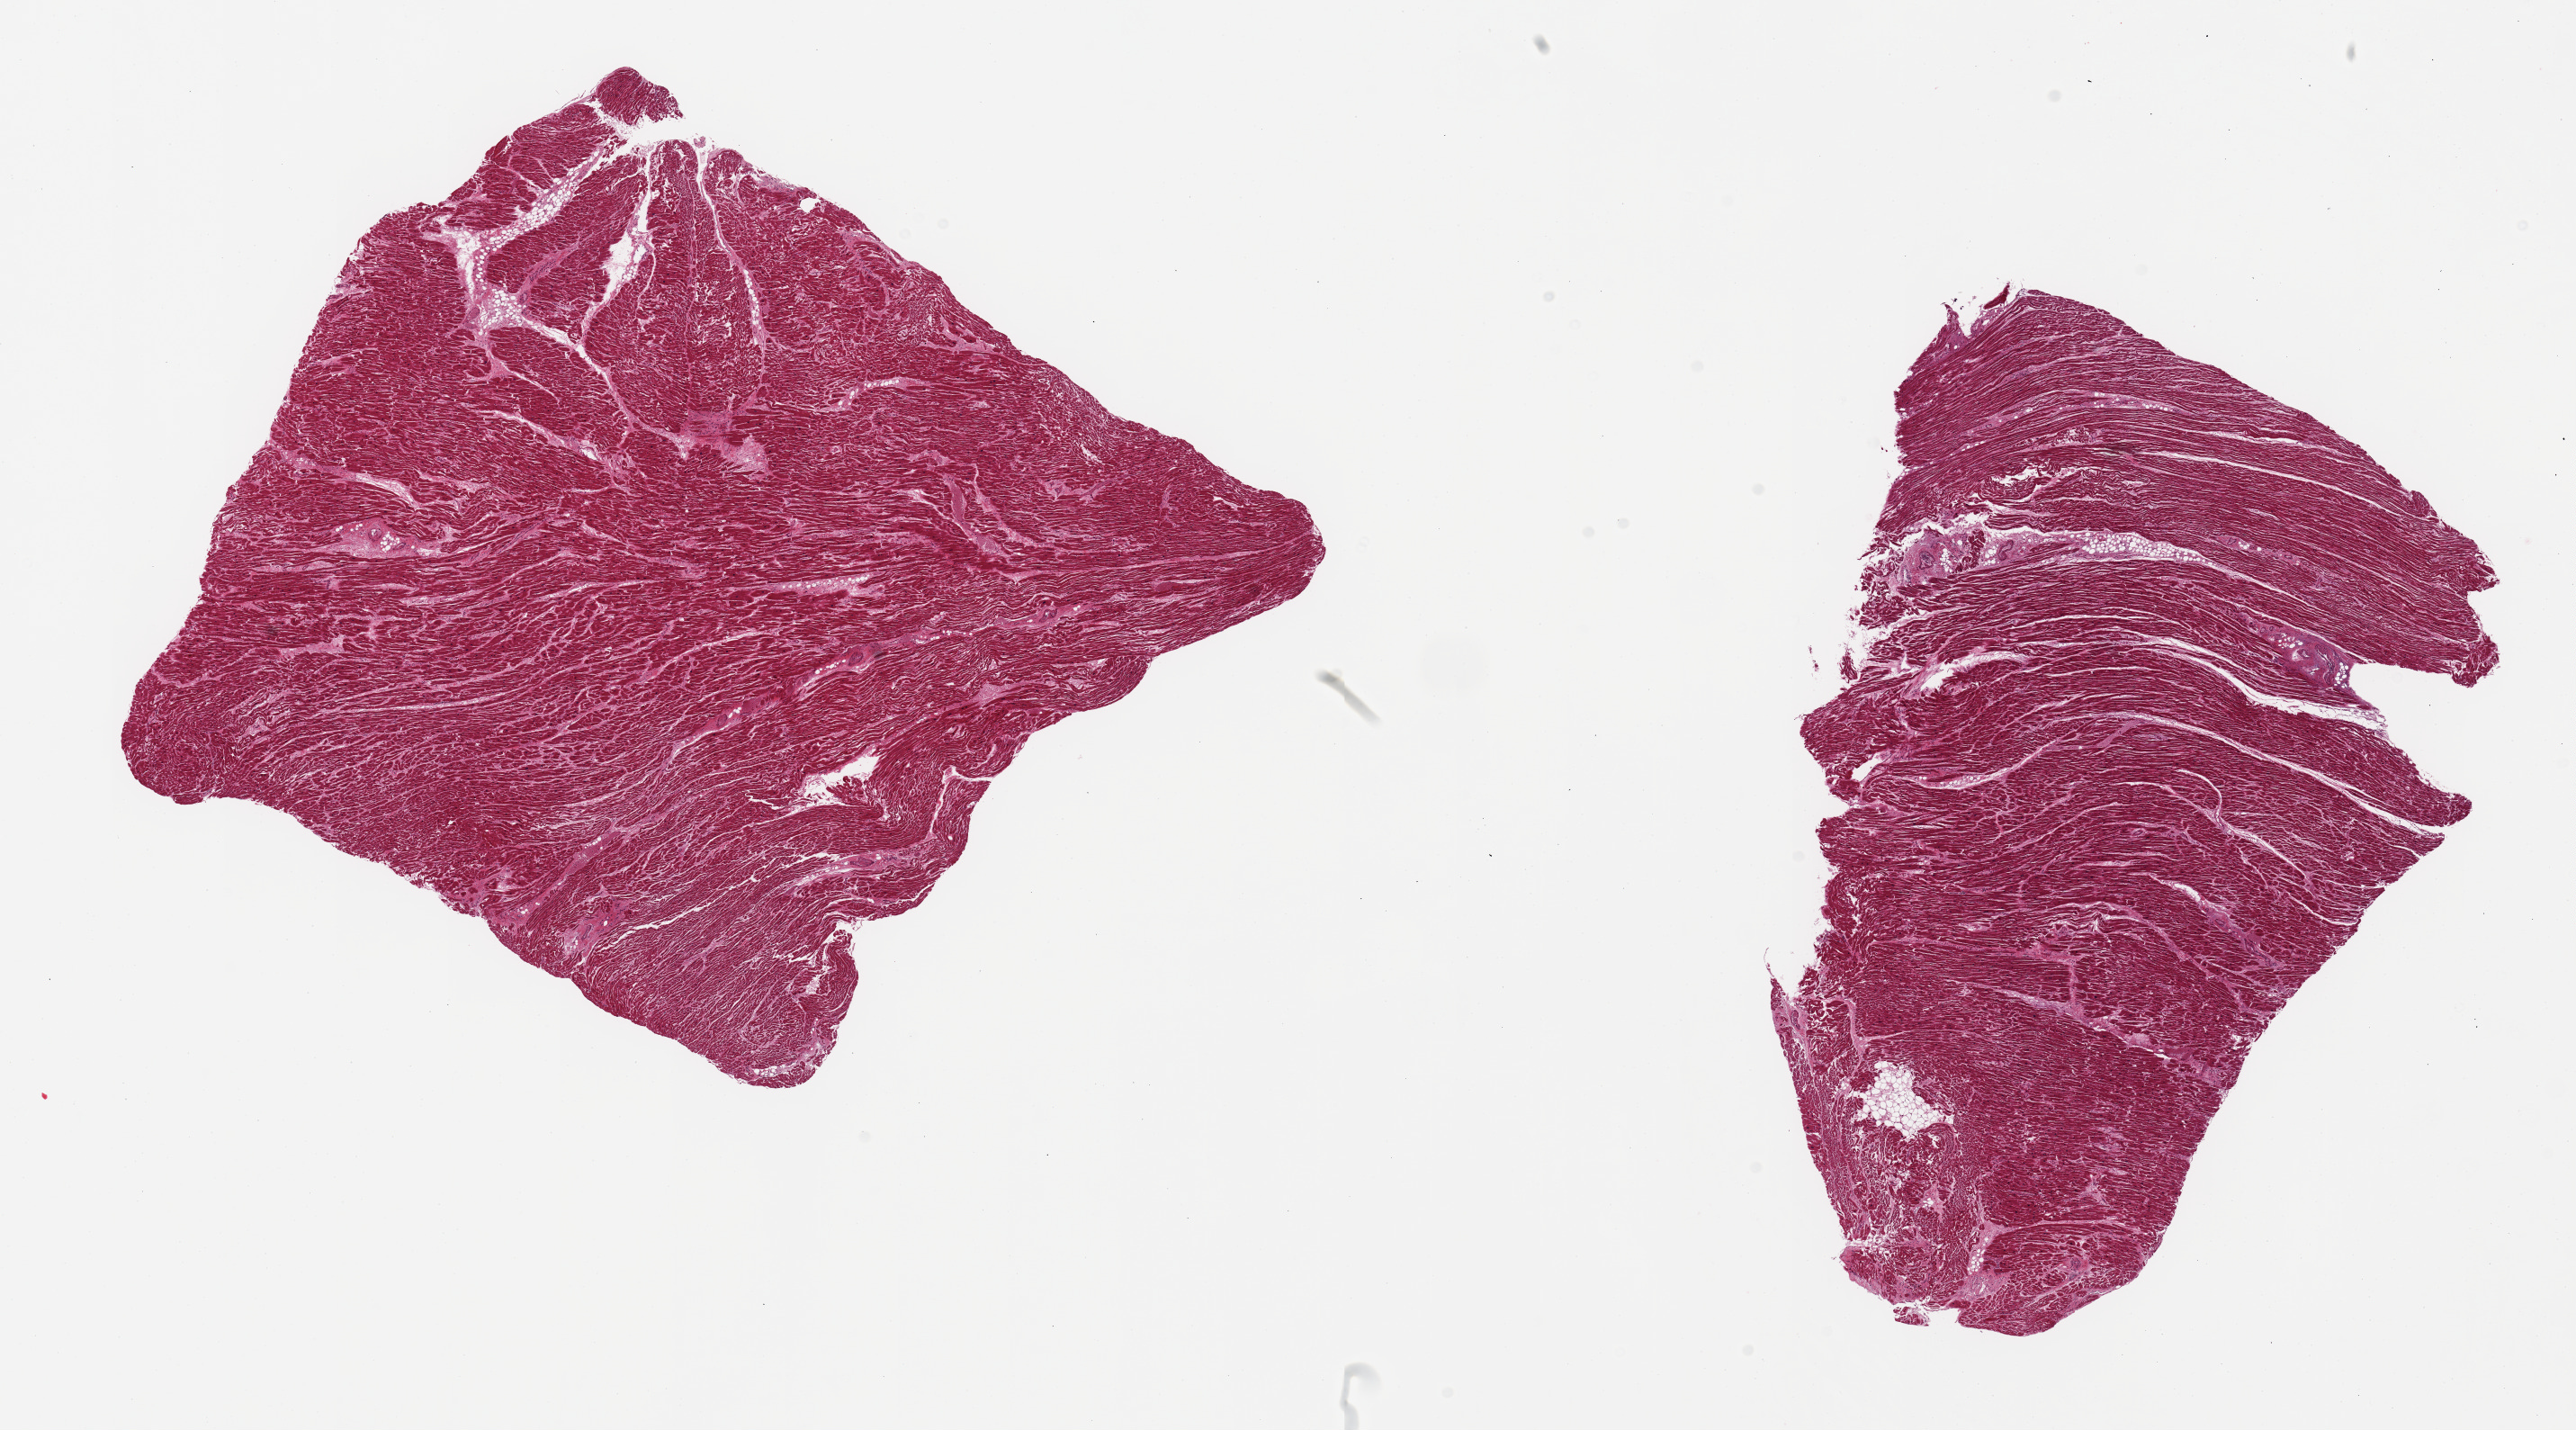
Digitized hematoxylin and eosin (H&E)-stained section, brightfield, a low-resolution overview of the entire scanned area, about 22.6 x 12.6 mm (from a 20x scan); PAXgene-fixed paraffin-embedded (PFPE) section; sampled site (target tissue): heart; tissue donor sample. Donor: male.
Pathologist's review note for this sample: 2 pieces; mild to moderate autolysis, some fragmentation of fibers, hypertrophy.